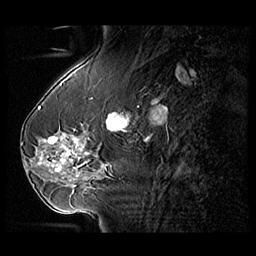
Breast MRI (dynamic contrast-enhanced), one sagittal slice. Position 40 of 104 along the scan axis. 3 images stored at this slice position (order not interpretable as contrast timing). 1.5 T. TE 1.3 ms, TR 5.5 ms. 3 mm slice thickness. 256 × 256 image matrix. Patient: female, 54 years. From the clinical record (not read from this slice): setting: breast cancer imaged before/during neoadjuvant chemotherapy; receptor status: HR-positive, HER2-negative.
Structures marked on this image (semi-automatically segmented with operator editing):
- analysis volume of interest (the breast-tissue region the enhancement analysis was run in; not a lesion): bounding box (x1, y1, x2, y2) in pixels: (28, 127, 104, 182)
- tumour enhancement mask (voxels above the 140 % enhancement threshold inside the analysis volume of interest): (38, 136, 90, 172)